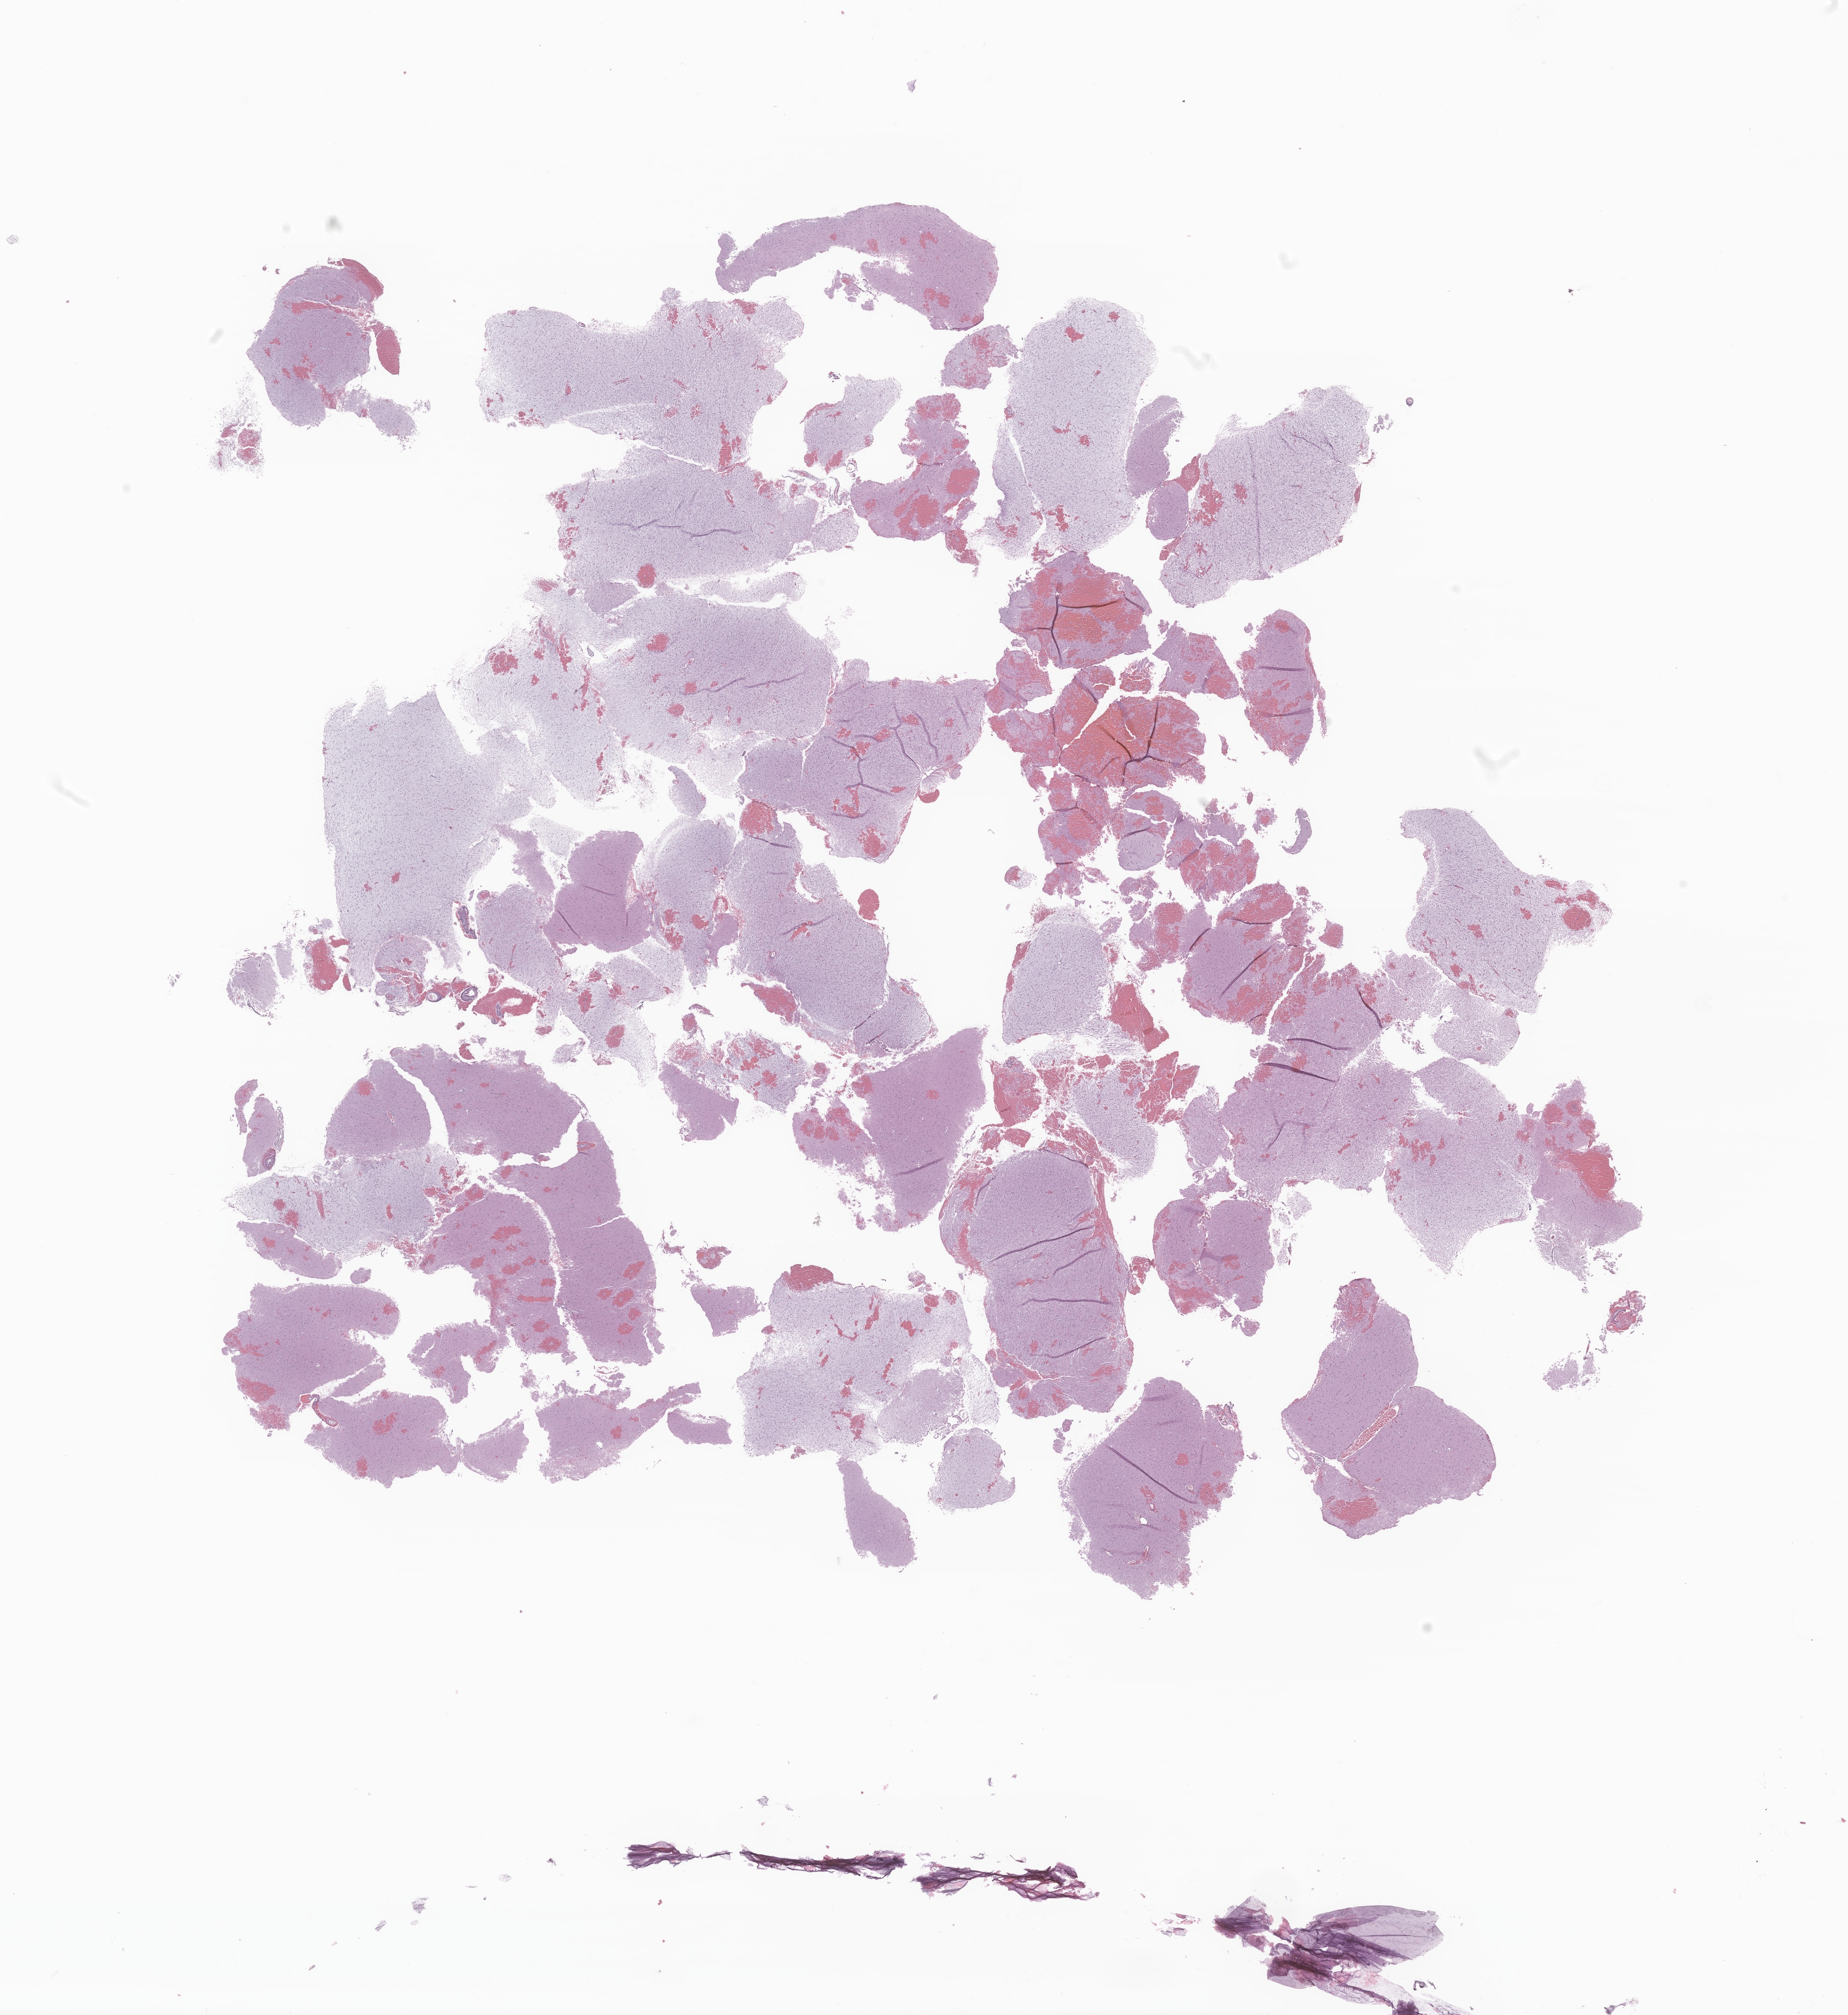
Whole-slide image, haematoxylin and eosin stain of tumor tissue from the frontal lobe, whole scanned area (about 17.8 x 19.4 mm) shown as a low-resolution overview. Formalin-fixed, paraffin-embedded (FFPE) tissue. Patient female; age 38 months (3 years 2 months).
Diagnosis (ICD-O-3 morphology term): Glioma, malignant.